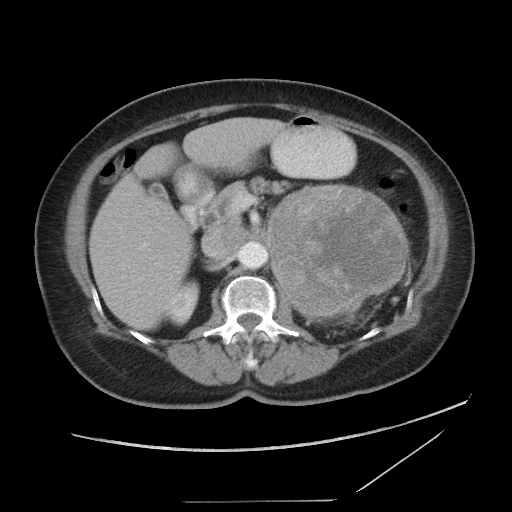
Contrast-enhanced abdominal CT, one axial slice. Slice 54 of 86 in the series (ordered by position). Reconstruction kernel STANDARD. 120 kVp. Intravenous contrast given. Soft-tissue window (W 400 / L 40 HU). 512 × 512 image matrix. Patient: female, 77 years. Case-level facts recorded for this patient, not image findings: diagnosis: adrenocortical carcinoma; tumour side: left adrenal; tumour size at pathology: 13.1 cm; Ki-67 index: 10 %.
Structures marked on this image (semi-automatic segmentation, software-assisted and operator-edited):
- mass: bounding box [x1, y1, x2, y2] px = [270, 188, 407, 316]